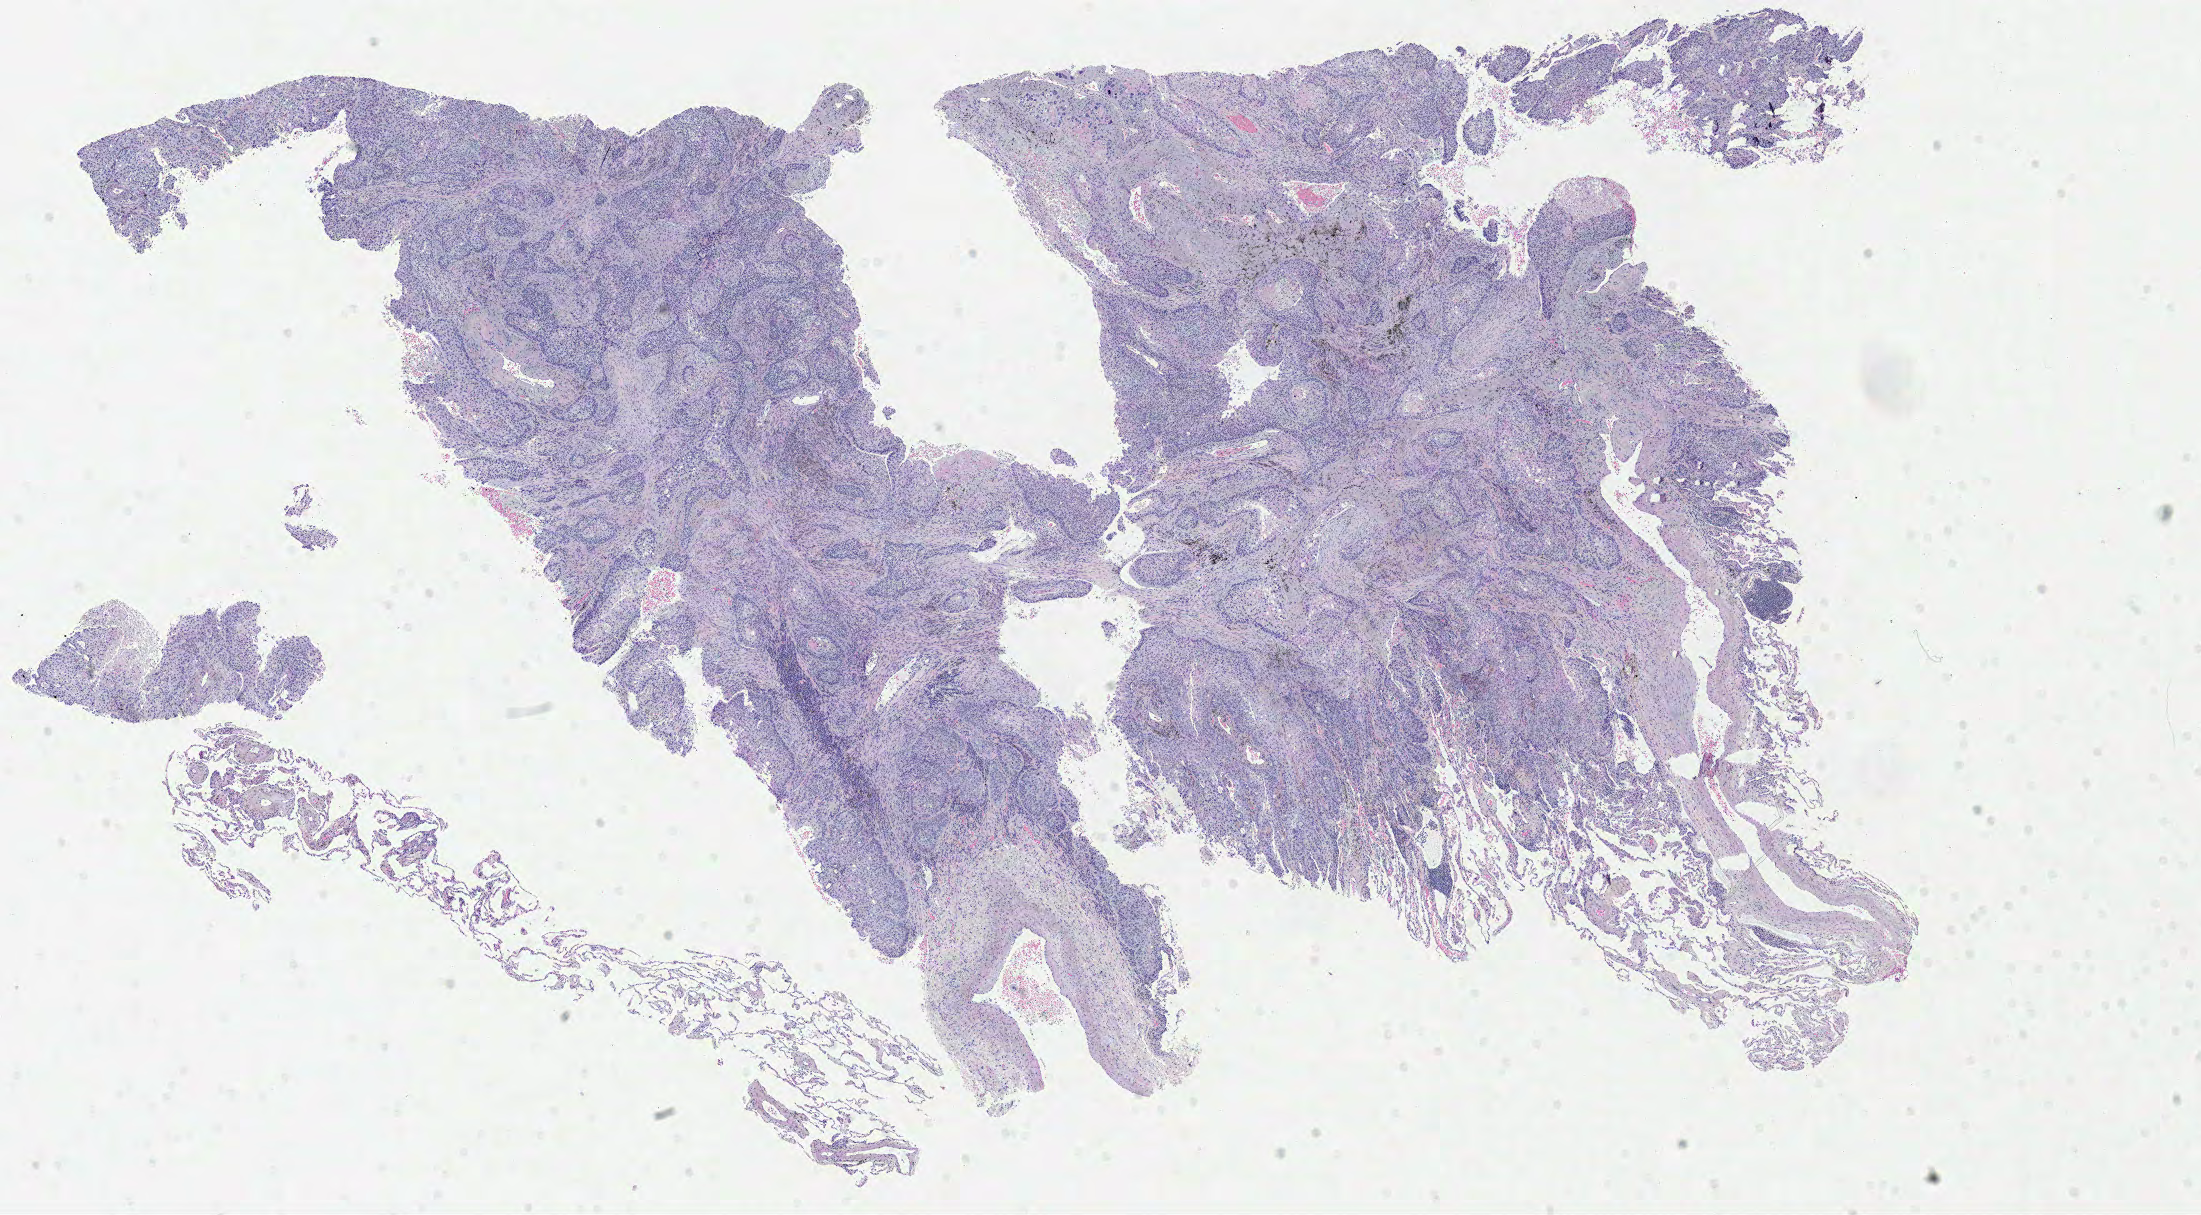
Digitized H&E tissue section (whole slide) — a low-resolution overview of the entire scanned area, about 17.3 x 9.6 mm; formalin-fixed paraffin-embedded (FFPE) diagnostic section; sample: primary tumour, lung. Patient: male, age at initial diagnosis 73 years.
- laterality: left
- AJCC pathologic stage: IIIB (6th edition)
- pathologic diagnosis: Squamous cell carcinoma, NOS (lower lobe, lung)